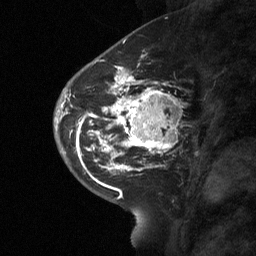
Breast MRI (dynamic contrast-enhanced), one sagittal slice. Slice 26 of 64 in the series (ordered by position). Dynamic contrast-enhanced study with each time point stored as its own series, time point 2 of 3 at this slice position (early post-contrast, ordered by acquisition time). 1.5 T. TE 4.8 ms, TR 27 ms. 256 × 256 image matrix. Female patient, age 42 years. Case-level facts recorded for this patient, not image findings: setting: breast cancer imaged before/during neoadjuvant chemotherapy; receptor status: triple-negative.
Outlined on this slice (semi-automatic segmentation, software-assisted and operator-edited):
- analysis volume of interest (the breast-tissue region the enhancement analysis was run in; not a lesion): bounding box [x1, y1, x2, y2] px = [115, 85, 177, 160]
- tumour enhancement mask (voxels above the 90 % enhancement threshold inside the analysis volume of interest): [115, 85, 177, 158]